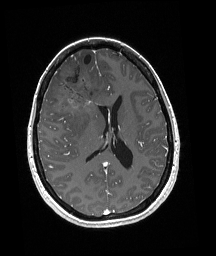
Brain MRI from a brain-tumour surgery series, one axial slice; position 85 of 192 along the scan axis; T1-weighted post-contrast; 216 × 256 image matrix, field of view 211 × 250 mm. From the clinical record (not read from this slice): histopathology: Oligodendroglioma; WHO grade: 3; IDH mutation: yes; tumour location: Right Frontal.
Annotated regions visible in this slice (outlined manually by an expert reader):
- tumour: bounding box (x1, y1, x2, y2) in pixels: (54, 77, 100, 115)